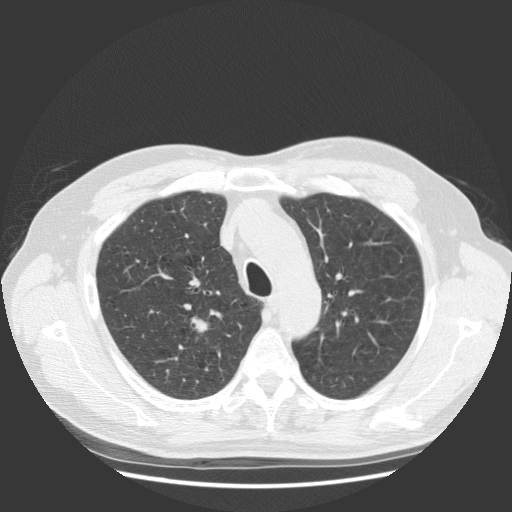
Low-dose screening chest CT, axial slice, baseline annual screen, lung window (W 1500 / L -600 HU), standard (soft-tissue) reconstruction kernel (STANDARD), slice 96 of 131 in the series, 512 × 512 image matrix. Male participant, aged 63 years at enrolment. Current smoker at enrolment.
Expert reader's lesion annotation, bounding box [x1, y1, x2, y2] px = [154, 299, 228, 376]. The screening reader recorded 2 non-calcified nodules or masses ≥4 mm on this exam; which of them this box marks is not recorded. Official screen result: positive, change unspecified: nodule(s) >= 4 mm or enlarging nodule(s), mass(es), or other non-specific abnormalities suspicious for lung cancer. Participant outcome: lung cancer diagnosed 30 days after this screen — squamous cell carcinoma, NOS, right upper lobe, stage IIIB (AJCC 6th edition), 35 mm at pathology.